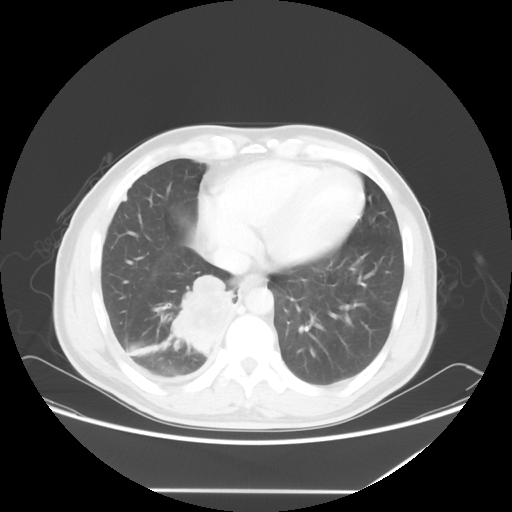
Chest CT, one axial slice; position 20 of 60 along the scan axis; lung window (W 1500 / L -600 HU); 512 × 512 image matrix. Patient: male, 48 years. Case-level facts recorded for this patient, not image findings: clinical TNM (as recorded): T3 N3 M1a.
Annotated regions visible in this slice (bounding box drawn by a radiologist):
- lung tumour (recorded histology: squamous cell carcinoma): bounding box [x1, y1, x2, y2] px = [166, 271, 240, 361]